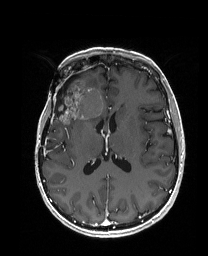
Brain MRI from a brain-tumour surgery series, one axial slice. Position 84 of 192 along the scan axis. T1-weighted post-contrast. 1 mm slice thickness. 208 × 256 image matrix, field of view 203 × 250 mm. Case-level facts recorded for this patient, not image findings: histopathology: Metastatic Carcinoma from Breast primary; tumour location: Right Frontal.
Outlined on this slice (manually delineated by an expert):
- previous resection cavity: bounding box (x1, y1, x2, y2) in pixels: (55, 78, 72, 115)
- tumour: (57, 83, 102, 124)